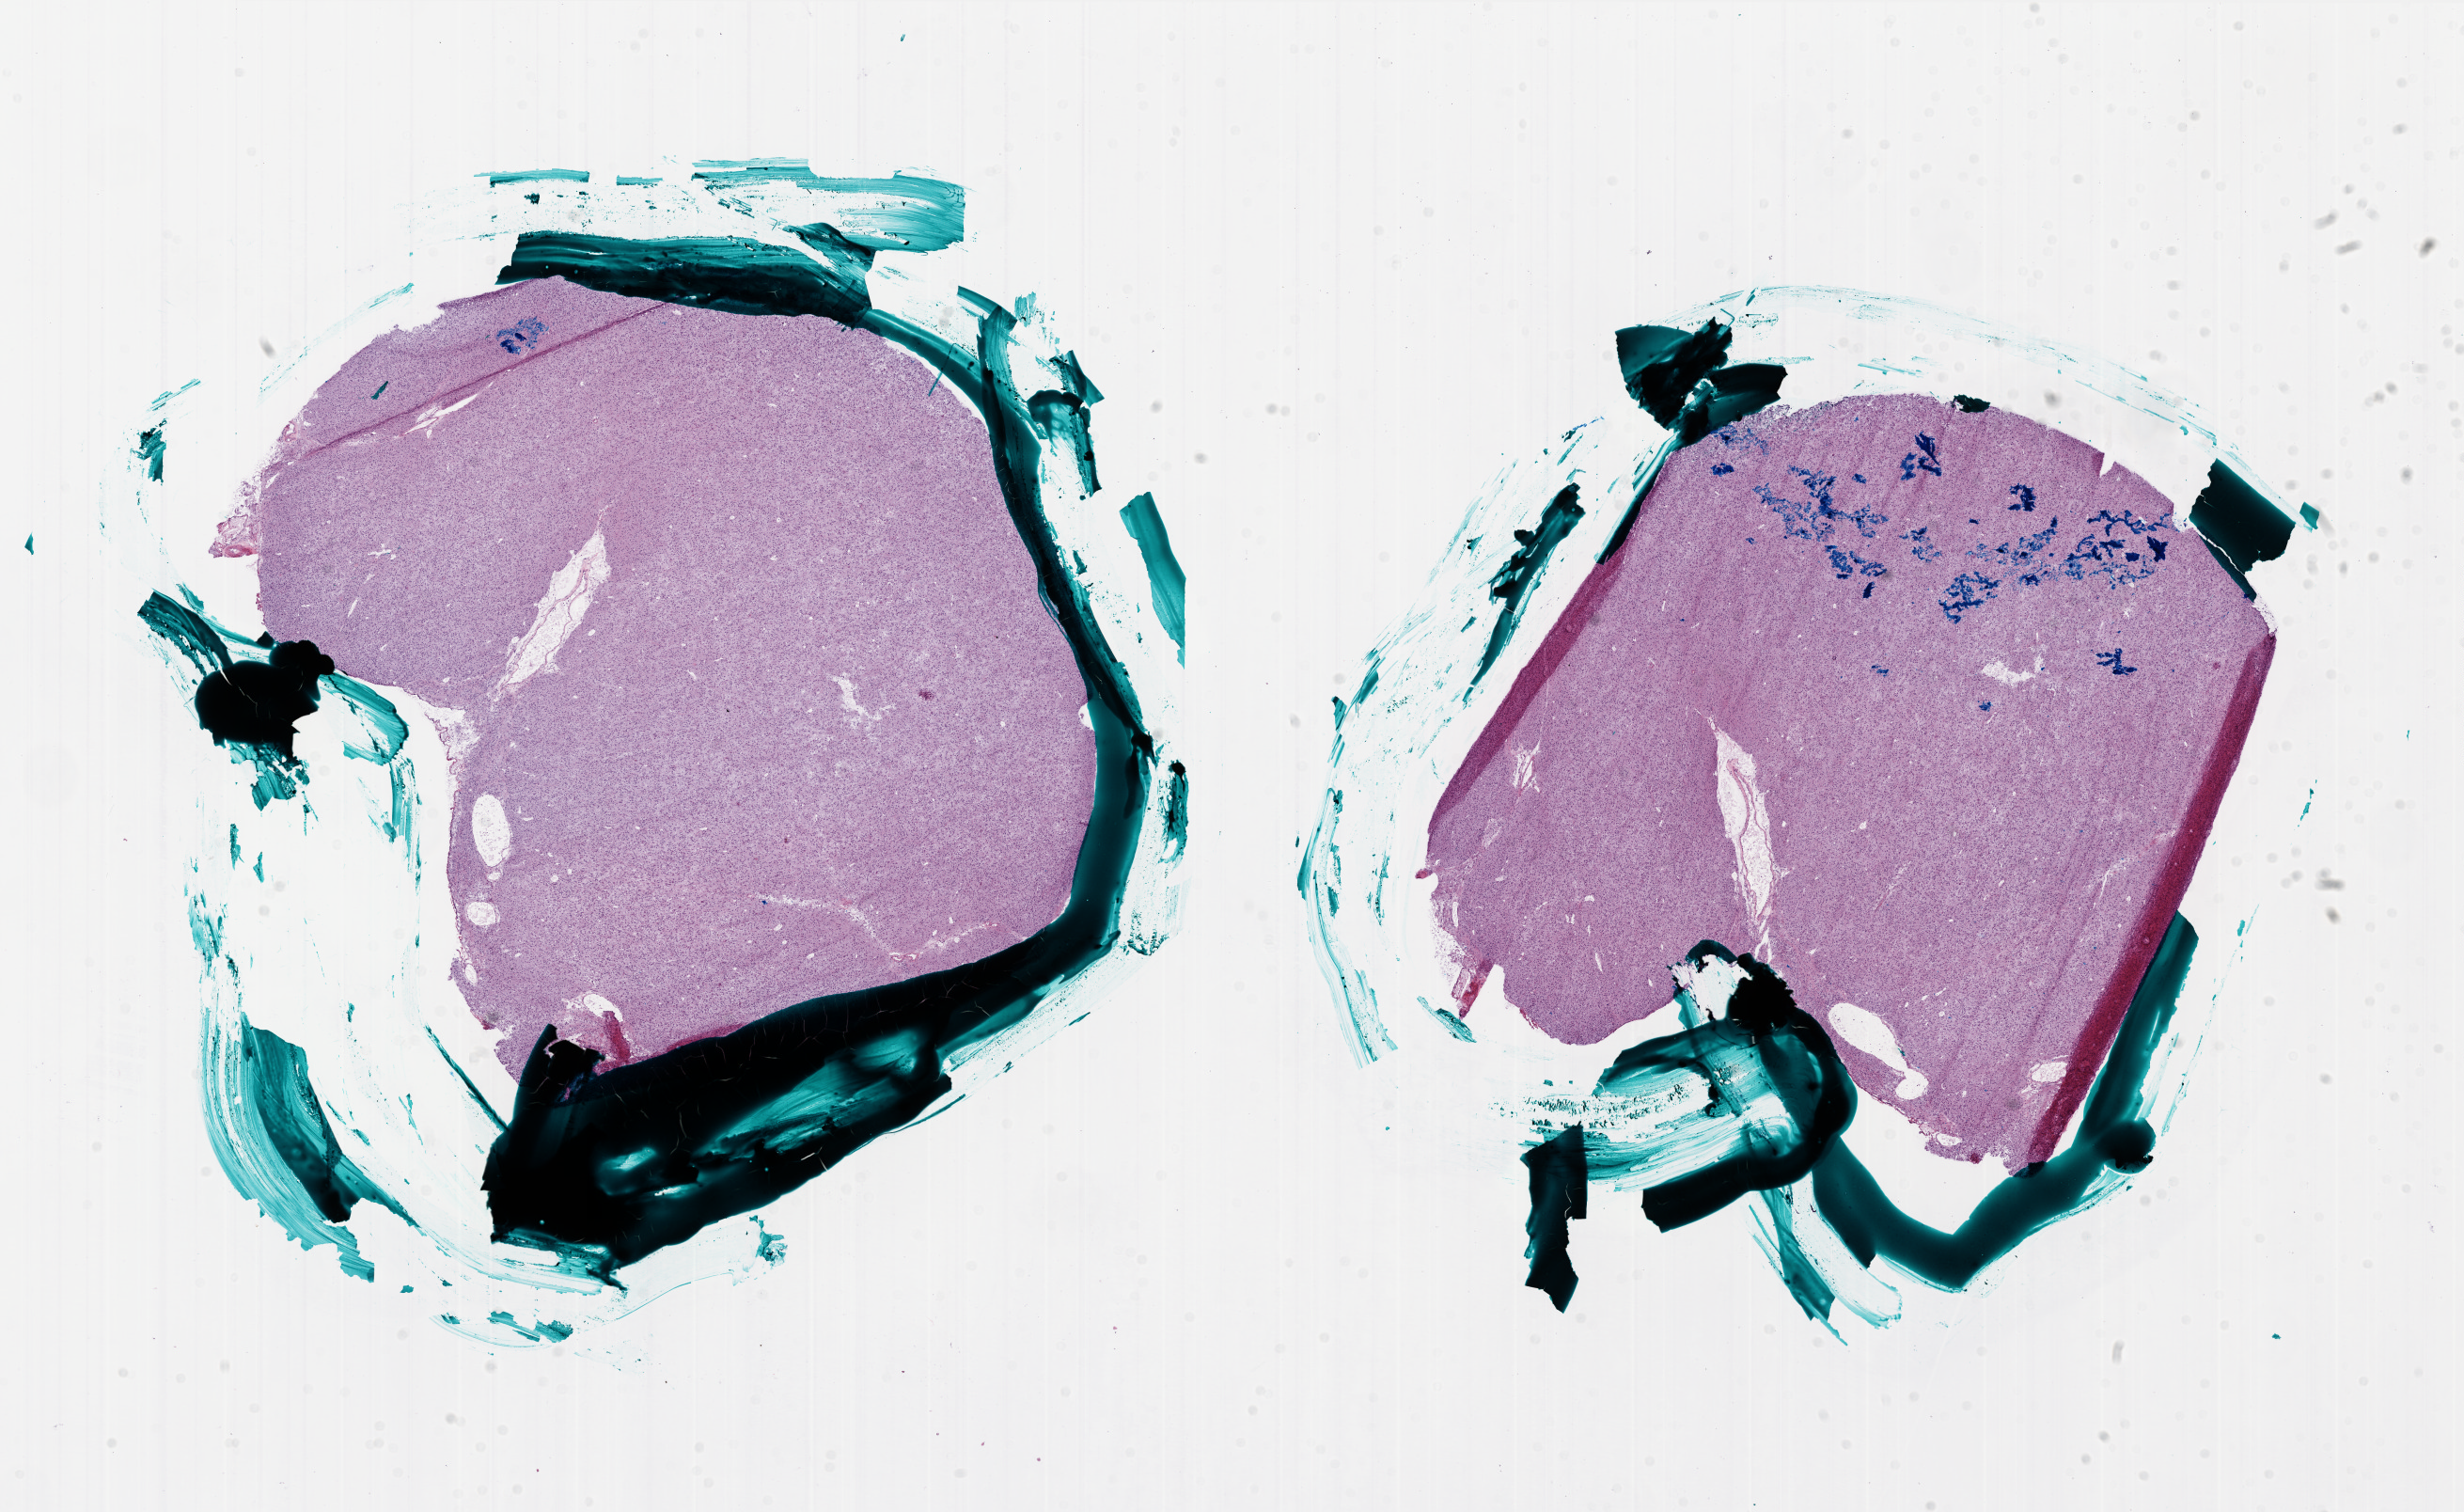
H&E-stained whole-slide image — shown as a low-resolution overview of the whole scanned area (about 21.0 x 12.9 mm), frozen section from the bottom of the tissue portion, brain, primary tumour sample. Female, age 52 years at initial diagnosis. Pathologist review of this section (percent, as recorded): tumour cells 100%, tumour nuclei 100%, normal cells 0%, stromal cells 0%, necrosis 0%.
Pathologic diagnosis: Glioblastoma.